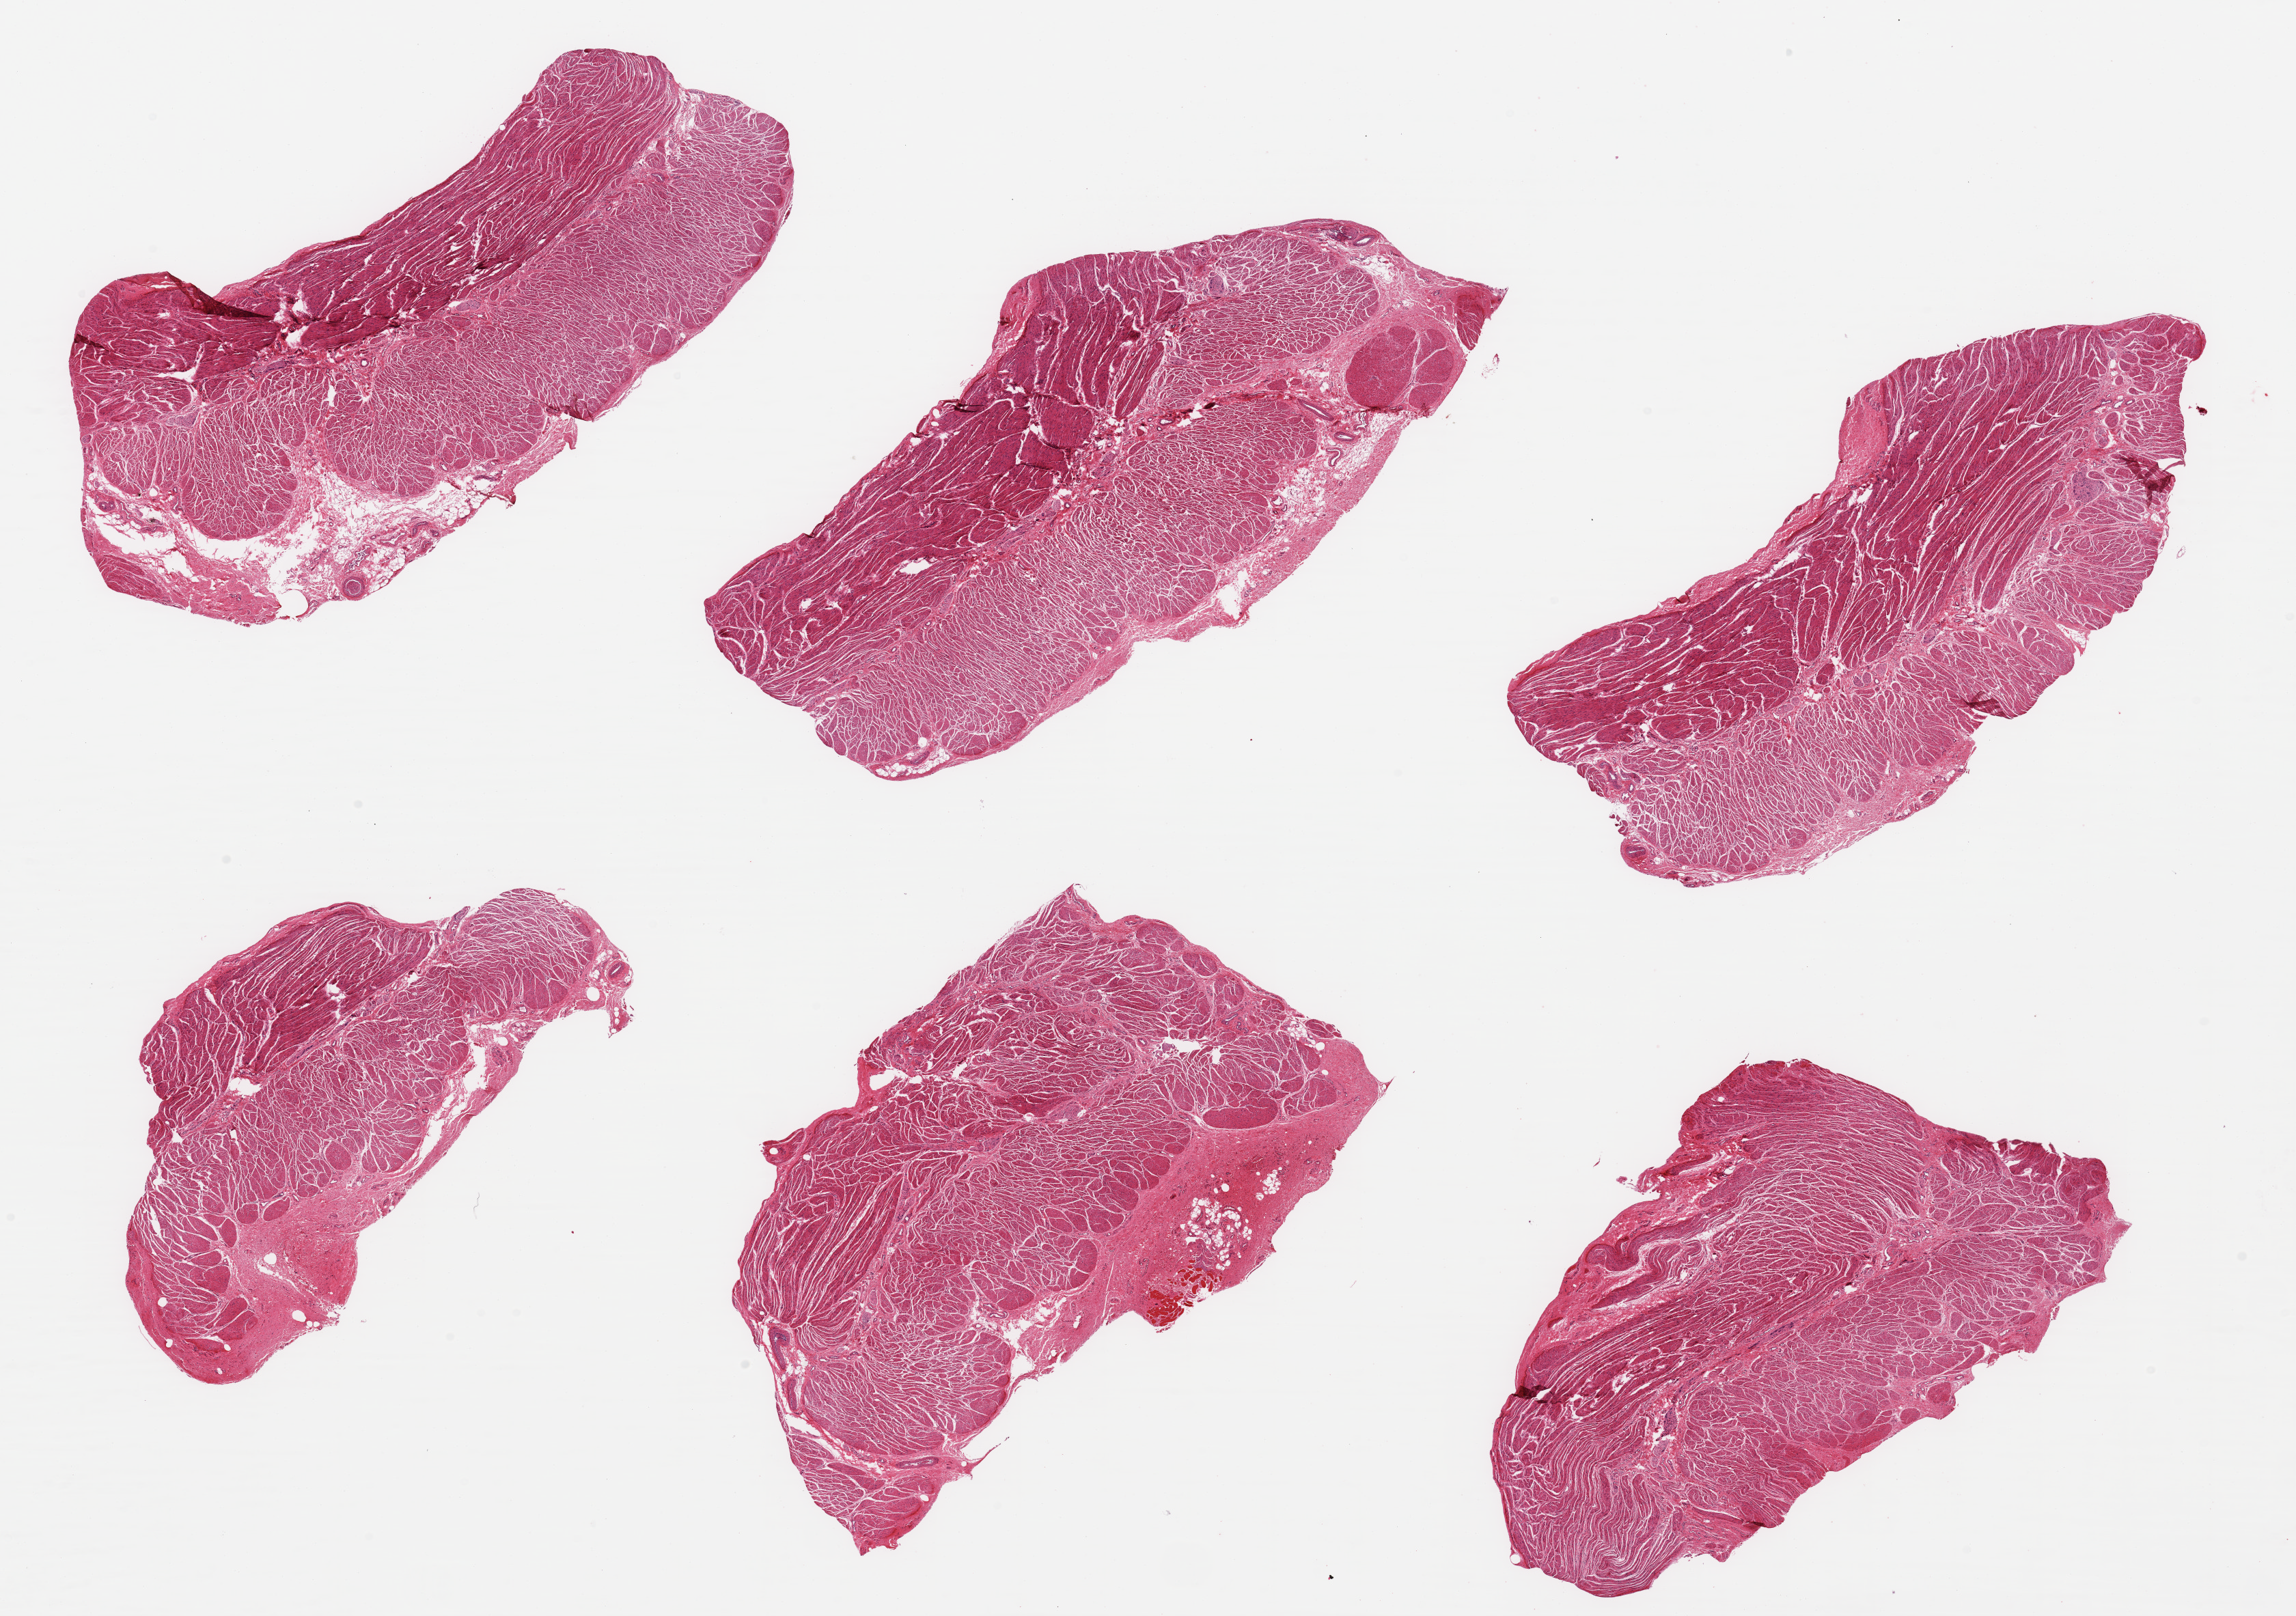
Digitized hematoxylin and eosin (H&E)-stained section — low-resolution overview of the scanned area, about 26.6 x 18.7 mm, PAXgene-fixed, paraffin-embedded tissue, sampled site (target tissue): gastroesophageal junction, donor tissue sample. Donor: female.
Review note (as recorded): 6 pieces; confirmed target muscularis and up to 1.5mm serosa with focal skeletal muscle fibers.